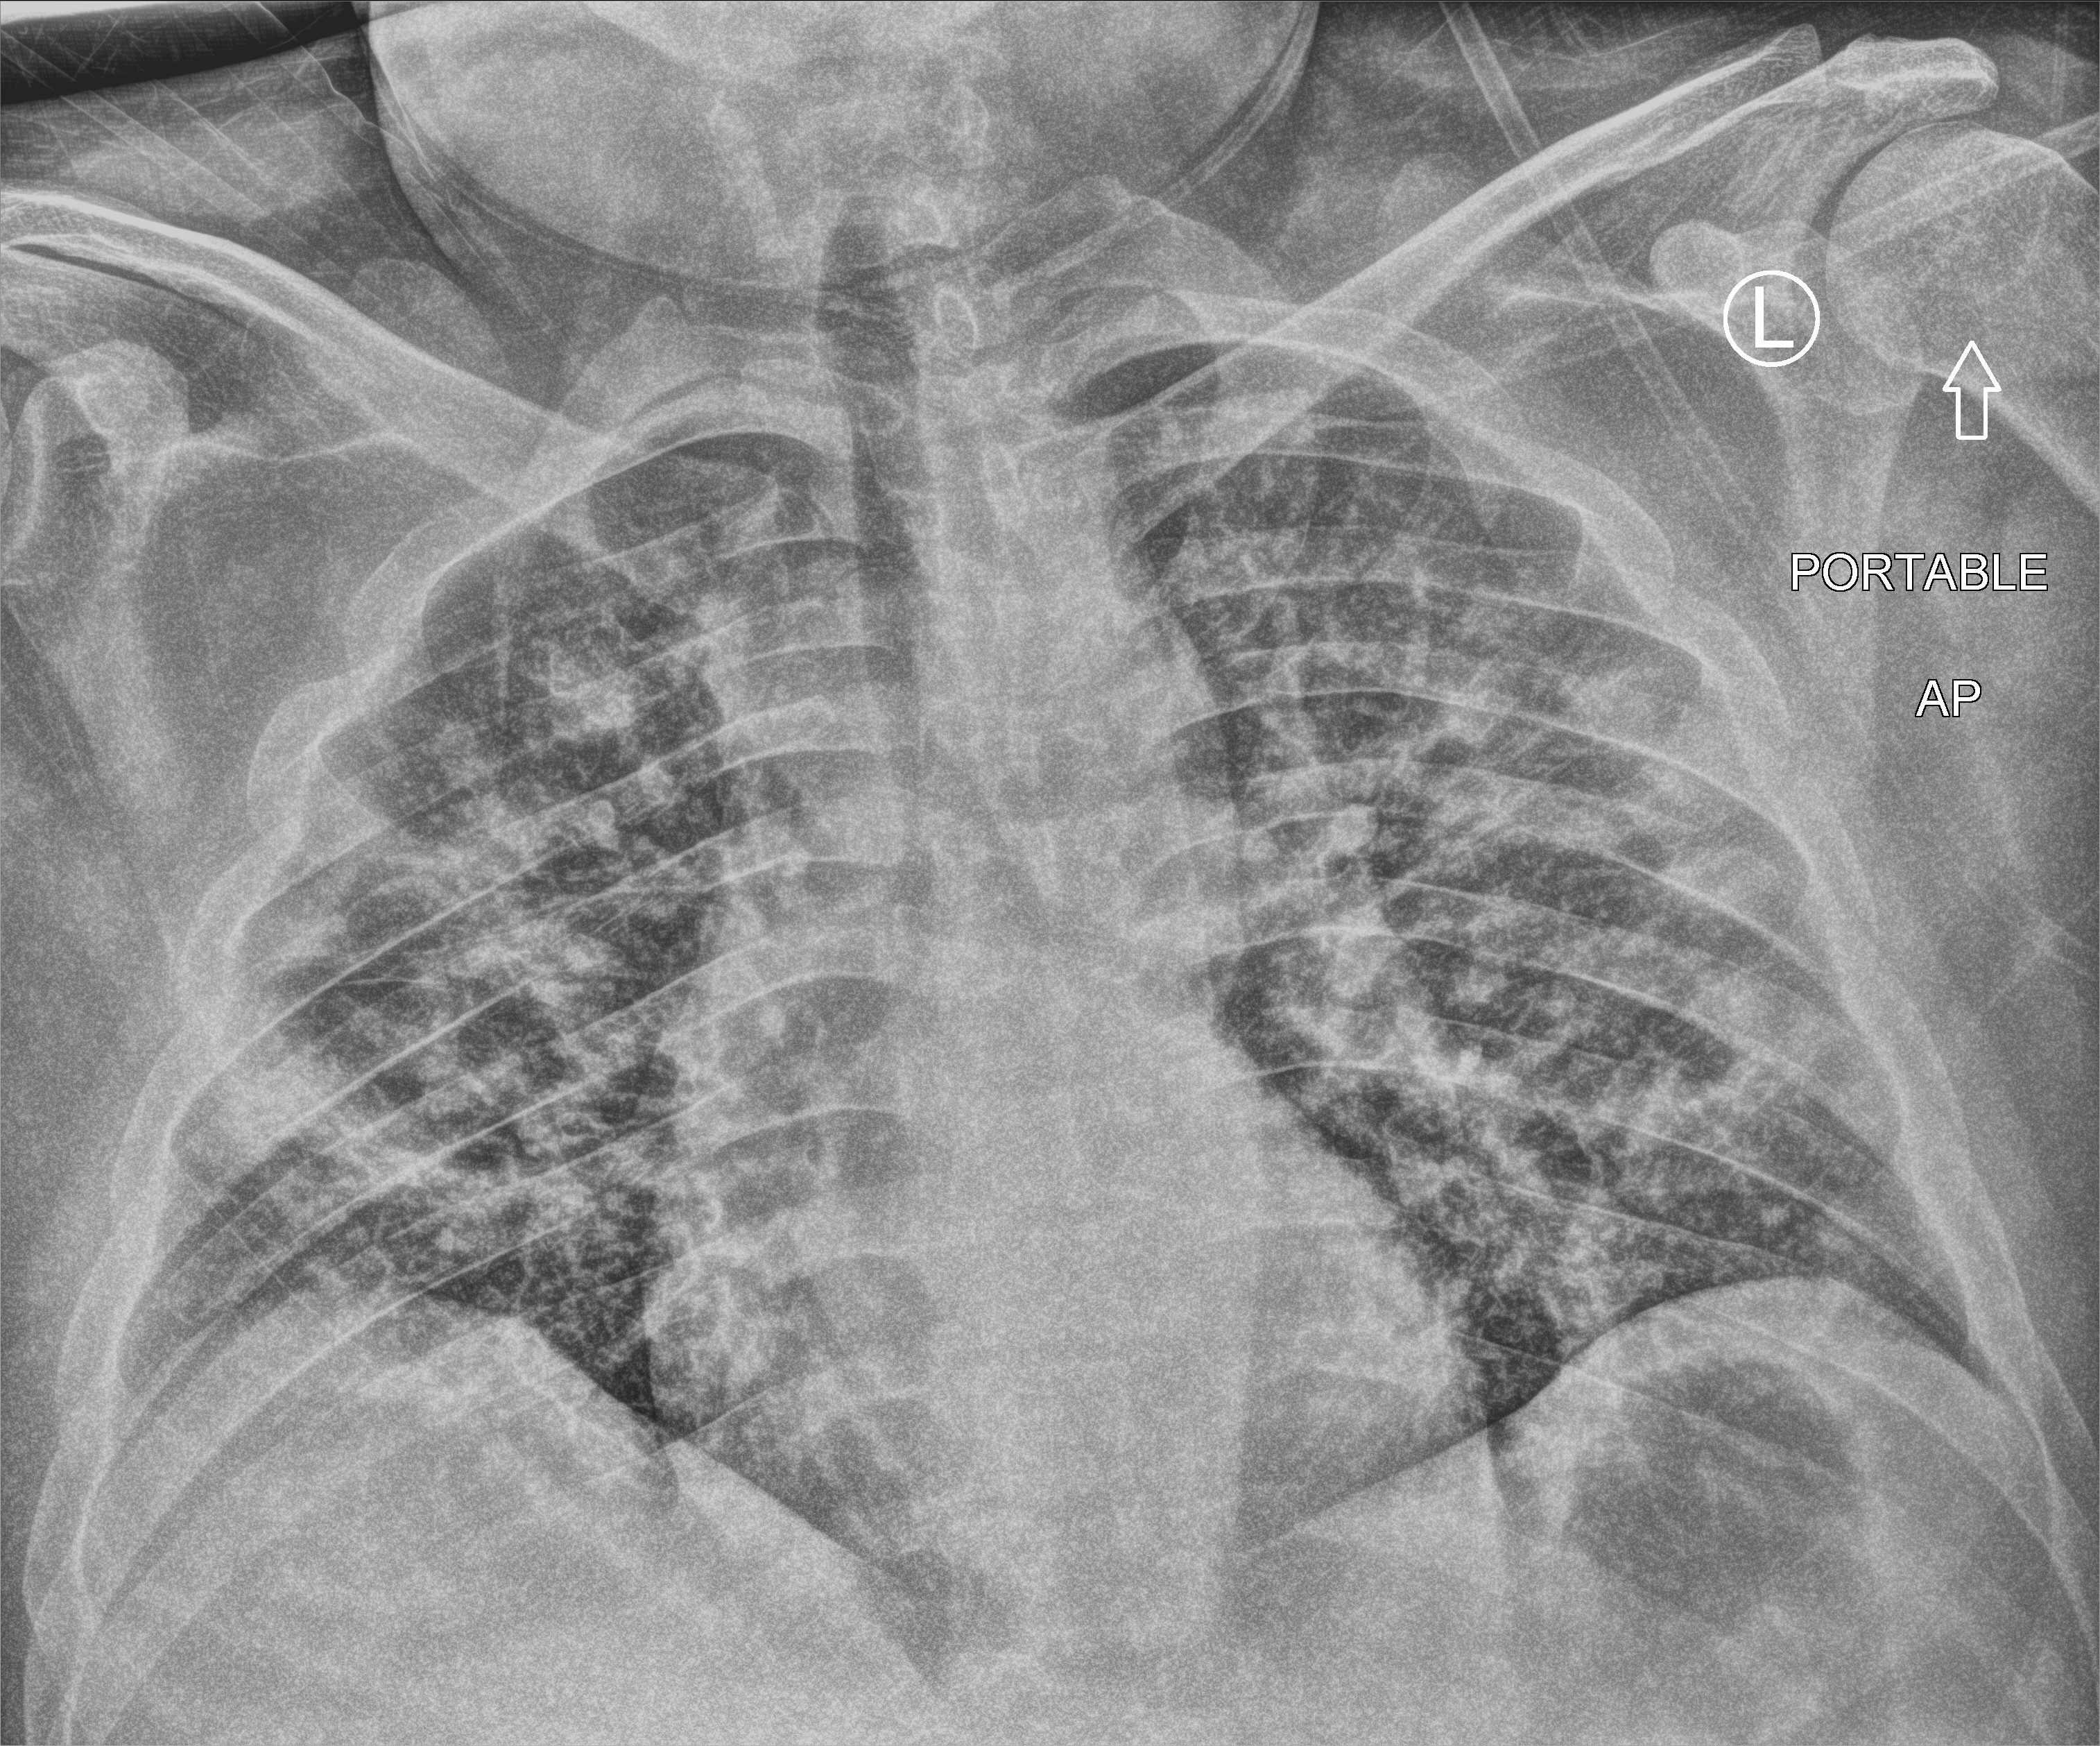
Bedside chest radiograph (computed radiography), anteroposterior (AP) projection. Patient hospitalised with COVID-19; female, aged 18–59 years.
Admission-level facts for this patient (not findings on this image; timing relative to this image not recorded): admitted to intensive care during this hospital stay: yes; mechanically ventilated during this hospital stay: yes.